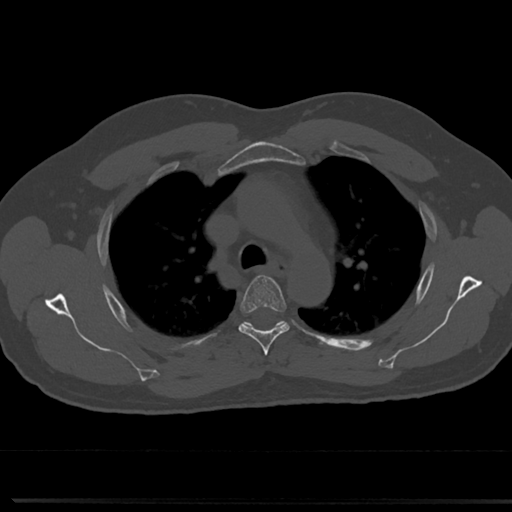
CT including the spine, one axial slice; slice 538 of 817 in the series (ordered by position); reconstruction kernel Br40s/3; bone window (W 1800 / L 400 HU); 0.5 mm slice thickness; 512 × 512 image matrix. Patient: male, 61 years. From the clinical record (not read from this slice): primary cancer: prostate.
Annotated regions visible in this slice (semi-automatically segmented with operator editing):
- T4 vertebra: box from (x=237, y=275) to (x=291, y=353) px
- T5 vertebra: (x=246, y=322)–(x=283, y=326)